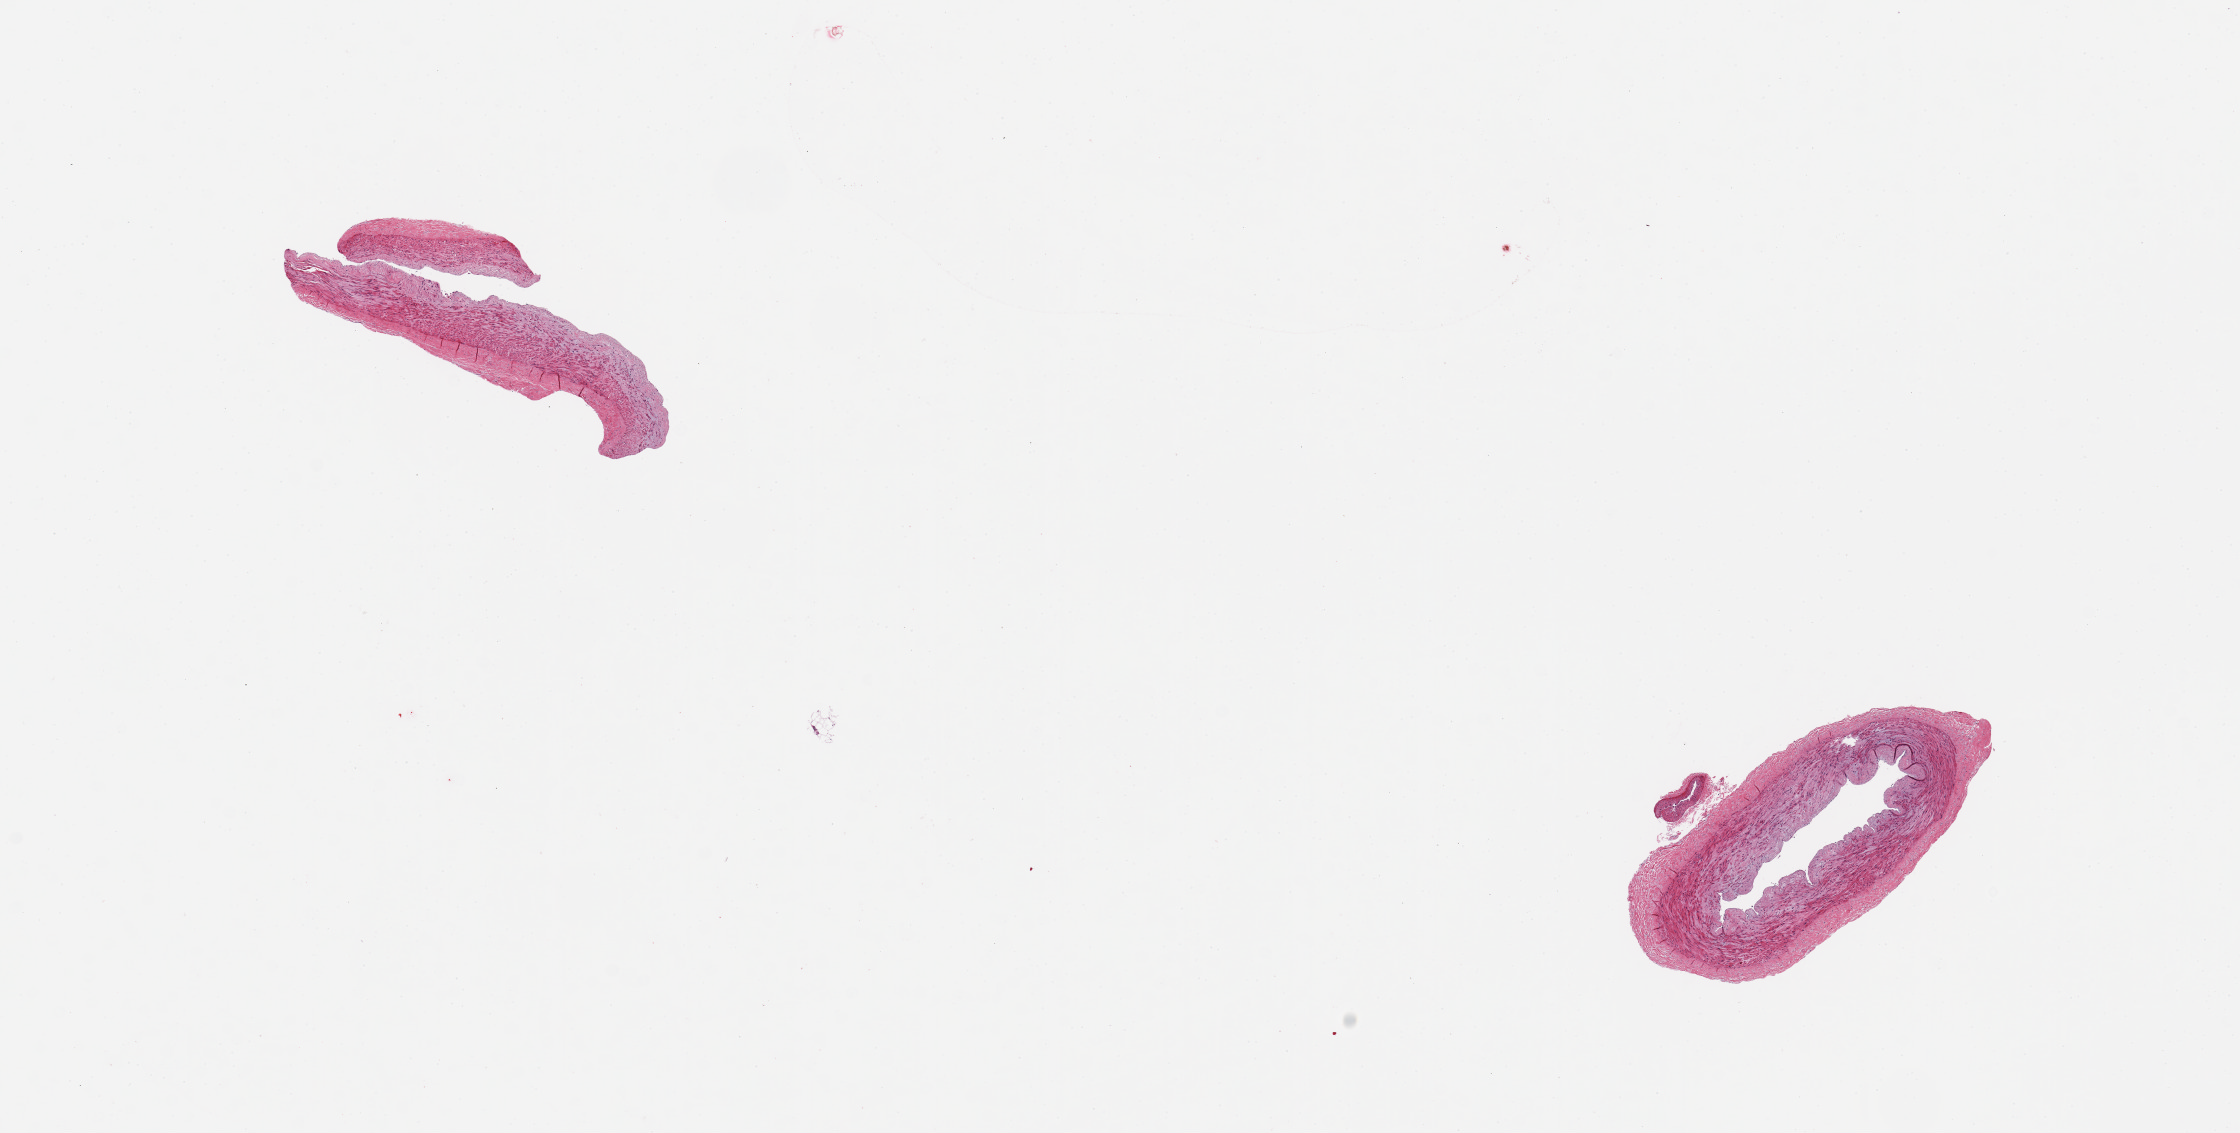
Digitized haematoxylin and eosin-stained section — low-resolution overview of the scanned area, about 17.7 x 9.0 mm (acquisition: 20x scan). PAXgene-fixed, paraffin-embedded tissue. Target tissue: tibial artery. Donor tissue sample. Donor: female.
* reviewer comment on this tissue sample: 2 pieces, no significant atherosis or adherent fat